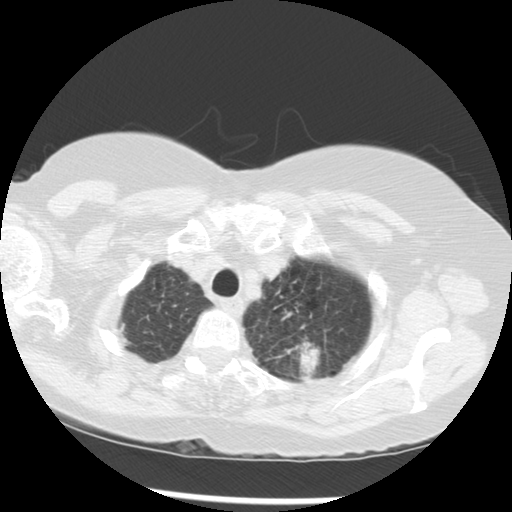
Low-dose screening chest CT, one axial slice. Position 246 of 283 along the scan axis. 120 kVp. Lung window (W 1500 / L -600 HU). 2.5 mm slice thickness. 512 × 512 image matrix, field of view 330 × 330 mm.
Structures marked on this image (outlined manually by an expert reader):
- lesion 1 (tumor, upper lobe of left lung): bounding box [x1, y1, x2, y2] px = [296, 343, 322, 376]